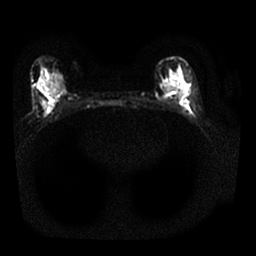
Breast MRI, one axial slice. Position 12 of 25 along the scan axis. Diffusion-weighted series; image 2 of 4 stored at this slice position (different b-values; order by instance number). 1.5 T. 4 mm slice thickness. 256 × 256 image matrix, field of view 310 × 310 mm. Female patient.
Annotated regions visible in this slice (manually delineated by an expert):
- tumour on diffusion-weighted imaging: box from (x=179, y=98) to (x=182, y=101) px